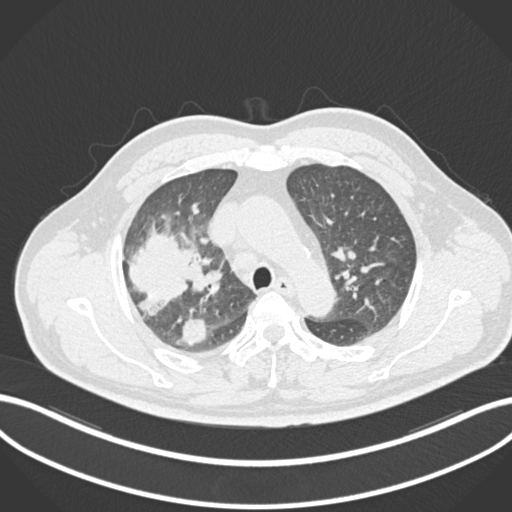
Chest CT, one axial slice. Slice 666 of 852 in the series (ordered by position). Reconstruction kernel B30f. Lung window (W 1500 / L -600 HU). 512 × 512 image matrix, field of view 400 × 400 mm. Patient: male, 55 years. From the clinical record (not read from this slice): clinical TNM (as recorded): T3 N2 M1.
Structures marked on this image (bounding box drawn by a radiologist):
- lung tumour (recorded histology: adenocarcinoma): box from (x=122, y=228) to (x=199, y=316) px